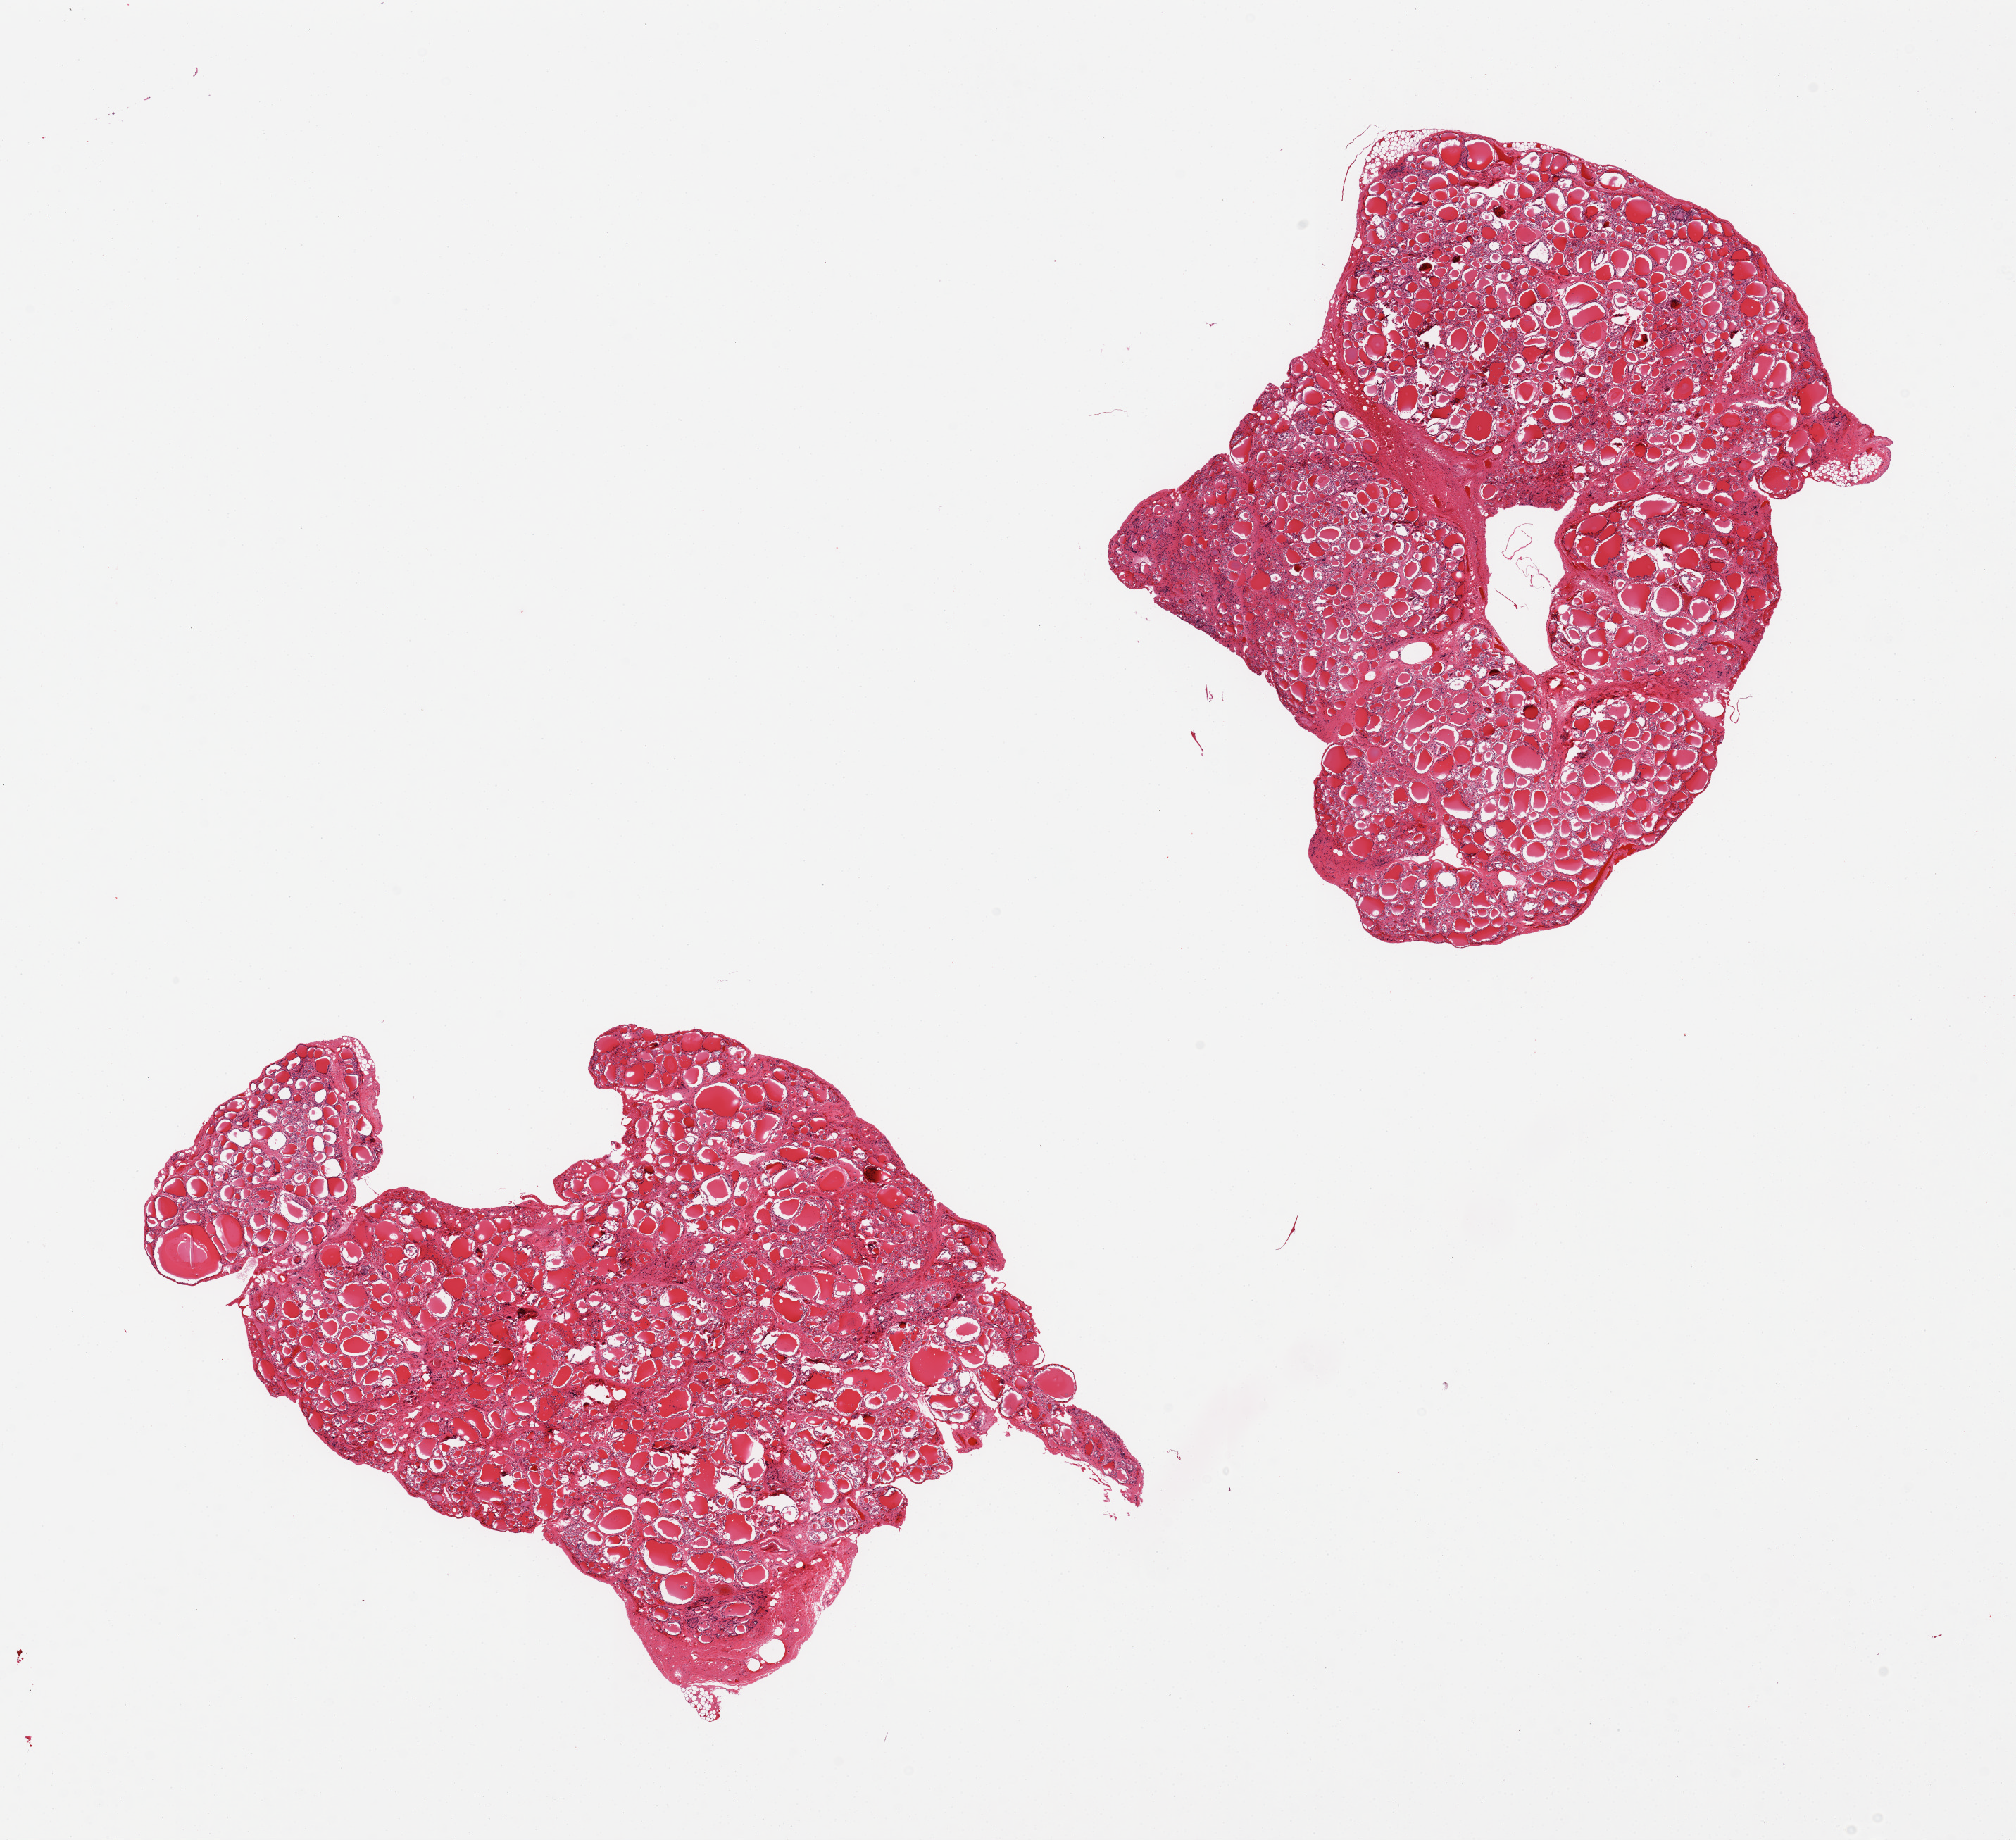
Whole-slide image, haematoxylin and eosin stain, a low-resolution overview of the entire scanned area, about 22.6 x 20.7 mm (from a 20x scan), PAXgene-fixed paraffin-embedded (PFPE) section, section of thyroid (target tissue), tissue donor sample. Male donor.
- pathologist's review note for this sample: 2 pieces, thyroid with moderate autolysis, not testis